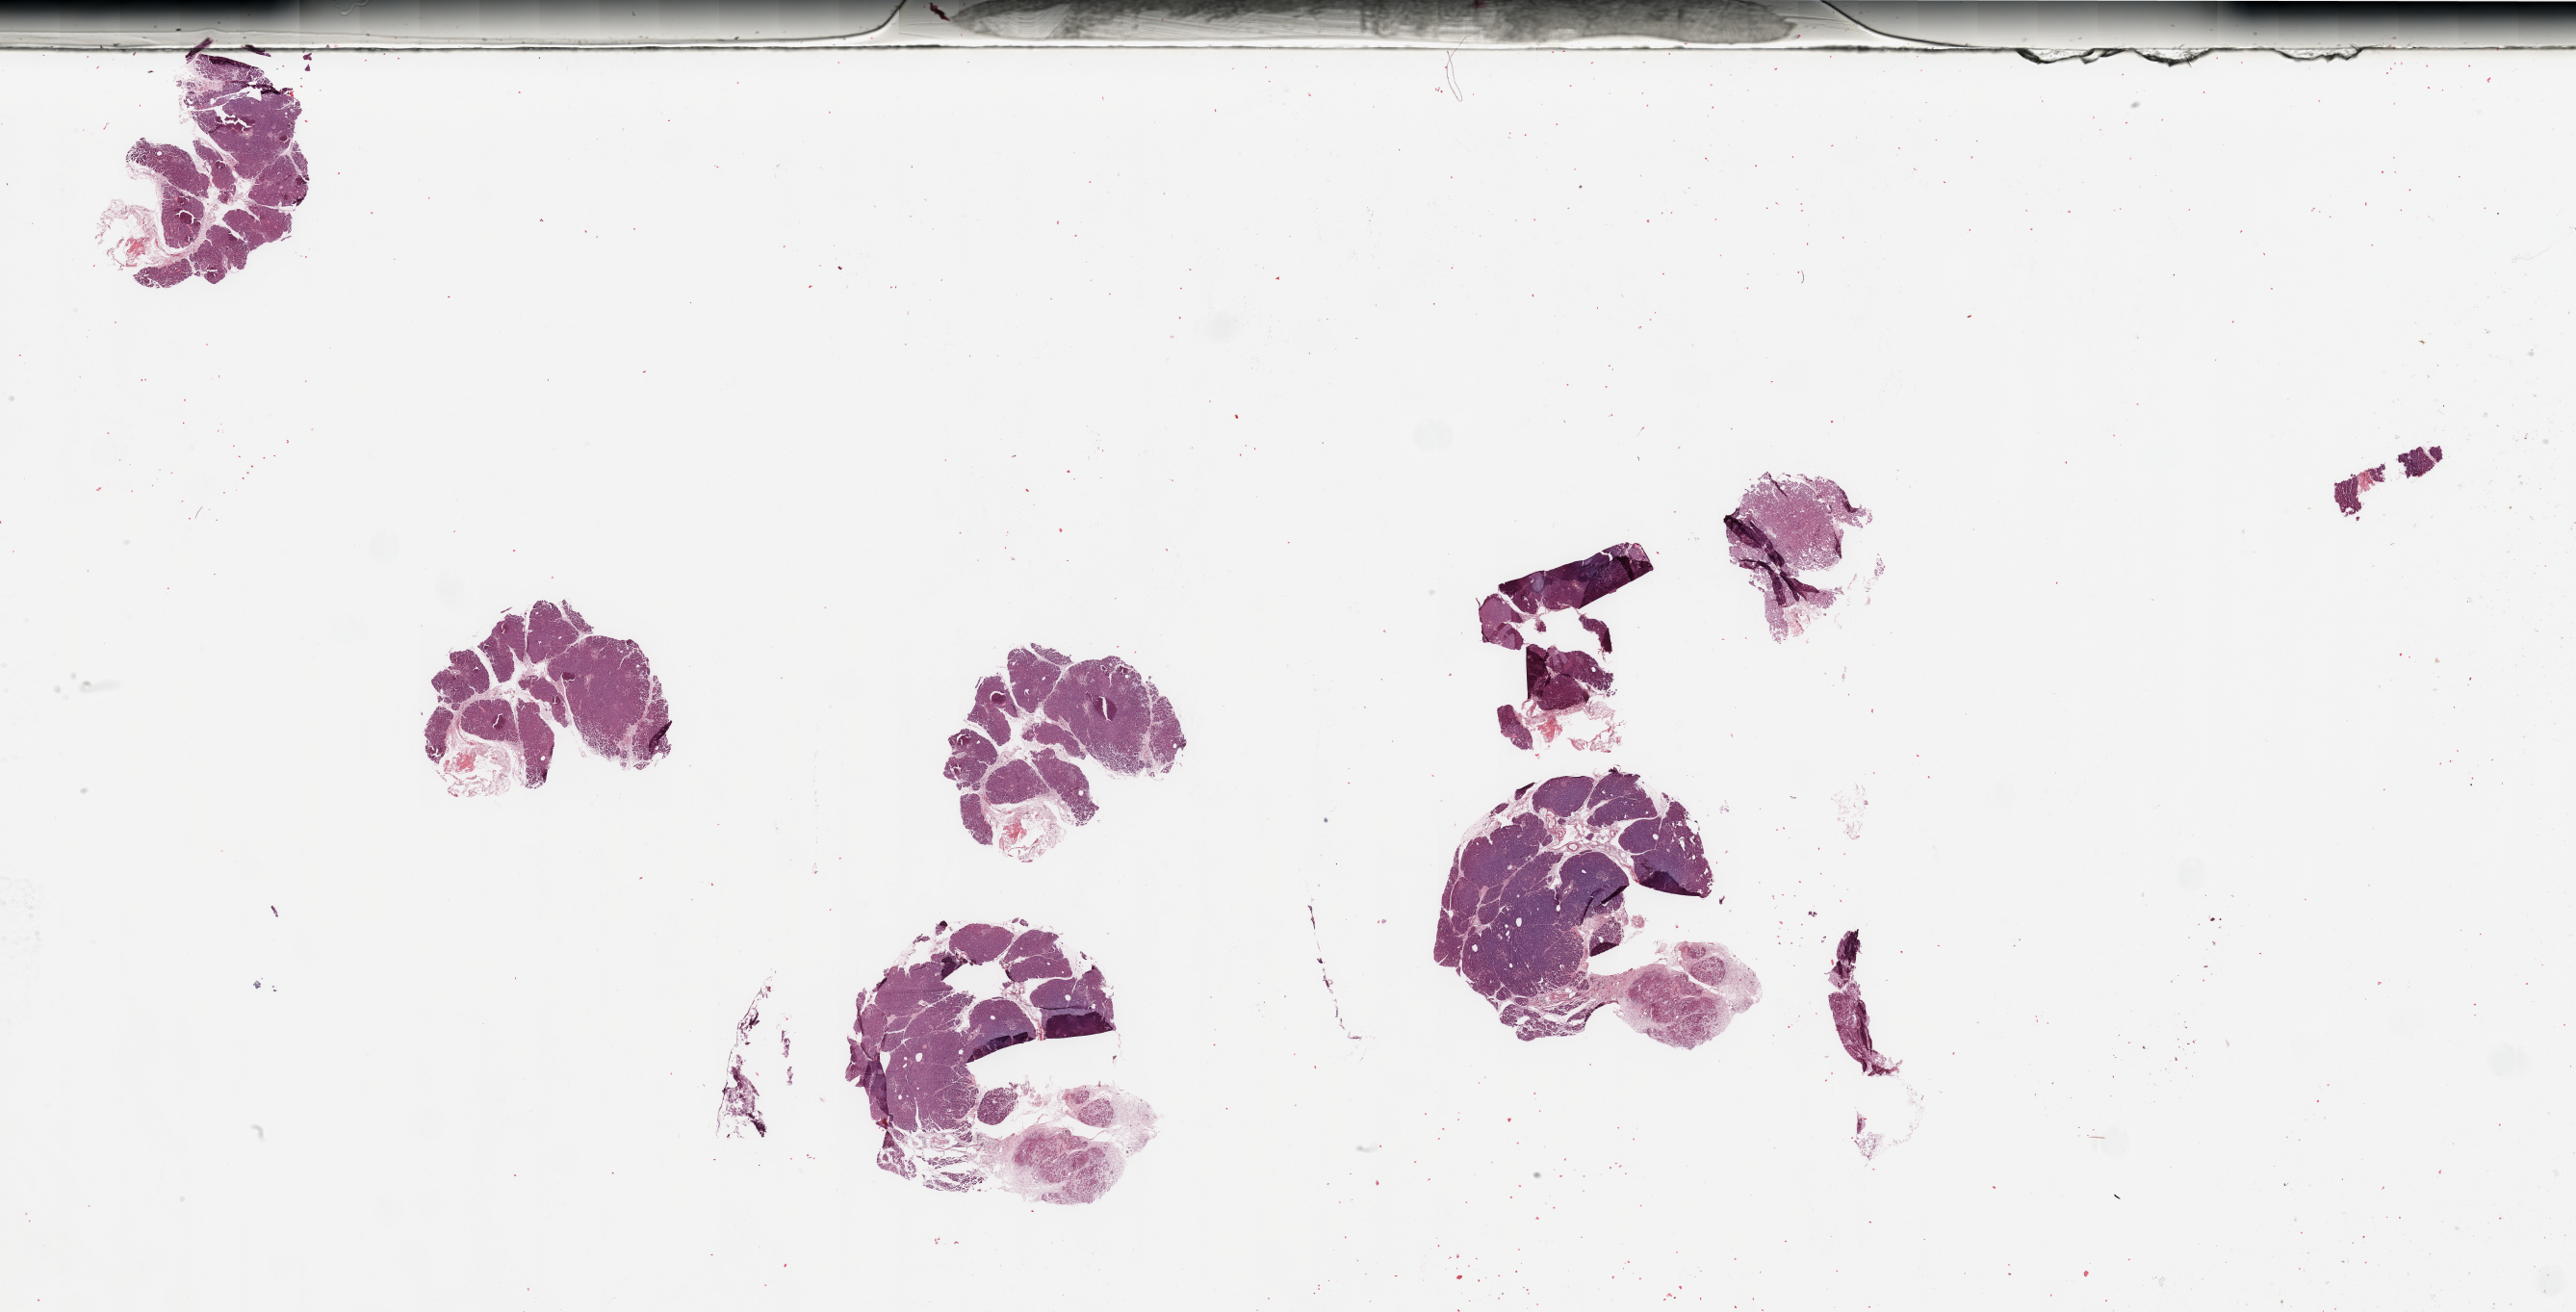
Digitized H&E tissue section (whole slide), whole scanned area (about 42.3 x 21.6 mm, acquisition: 20x scan) shown as a low-resolution overview; normal (non-tumour) tissue sample, sampled site: pancreas. Patient: female, age 54 years.
This section: normal (non-tumour) tissue from the same patient. Patient diagnosis: Infiltrating duct carcinoma, NOS.